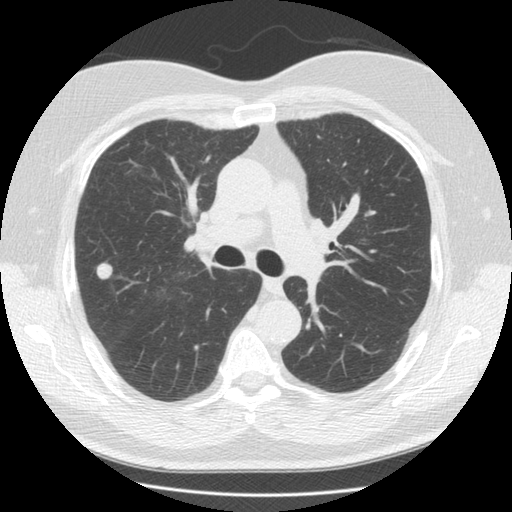
Low-dose screening chest CT, one axial slice. Position 90 of 146 along the scan axis. Lung window (W 1500 / L -600 HU). 2.5 mm slice thickness. 512 × 512 image matrix.
Outlined on this slice (outlined manually by an expert reader):
- lesion 1 (tumor, upper lobe of right lung): bounding box <96,262,114,280> (left, top, right, bottom; pixels)